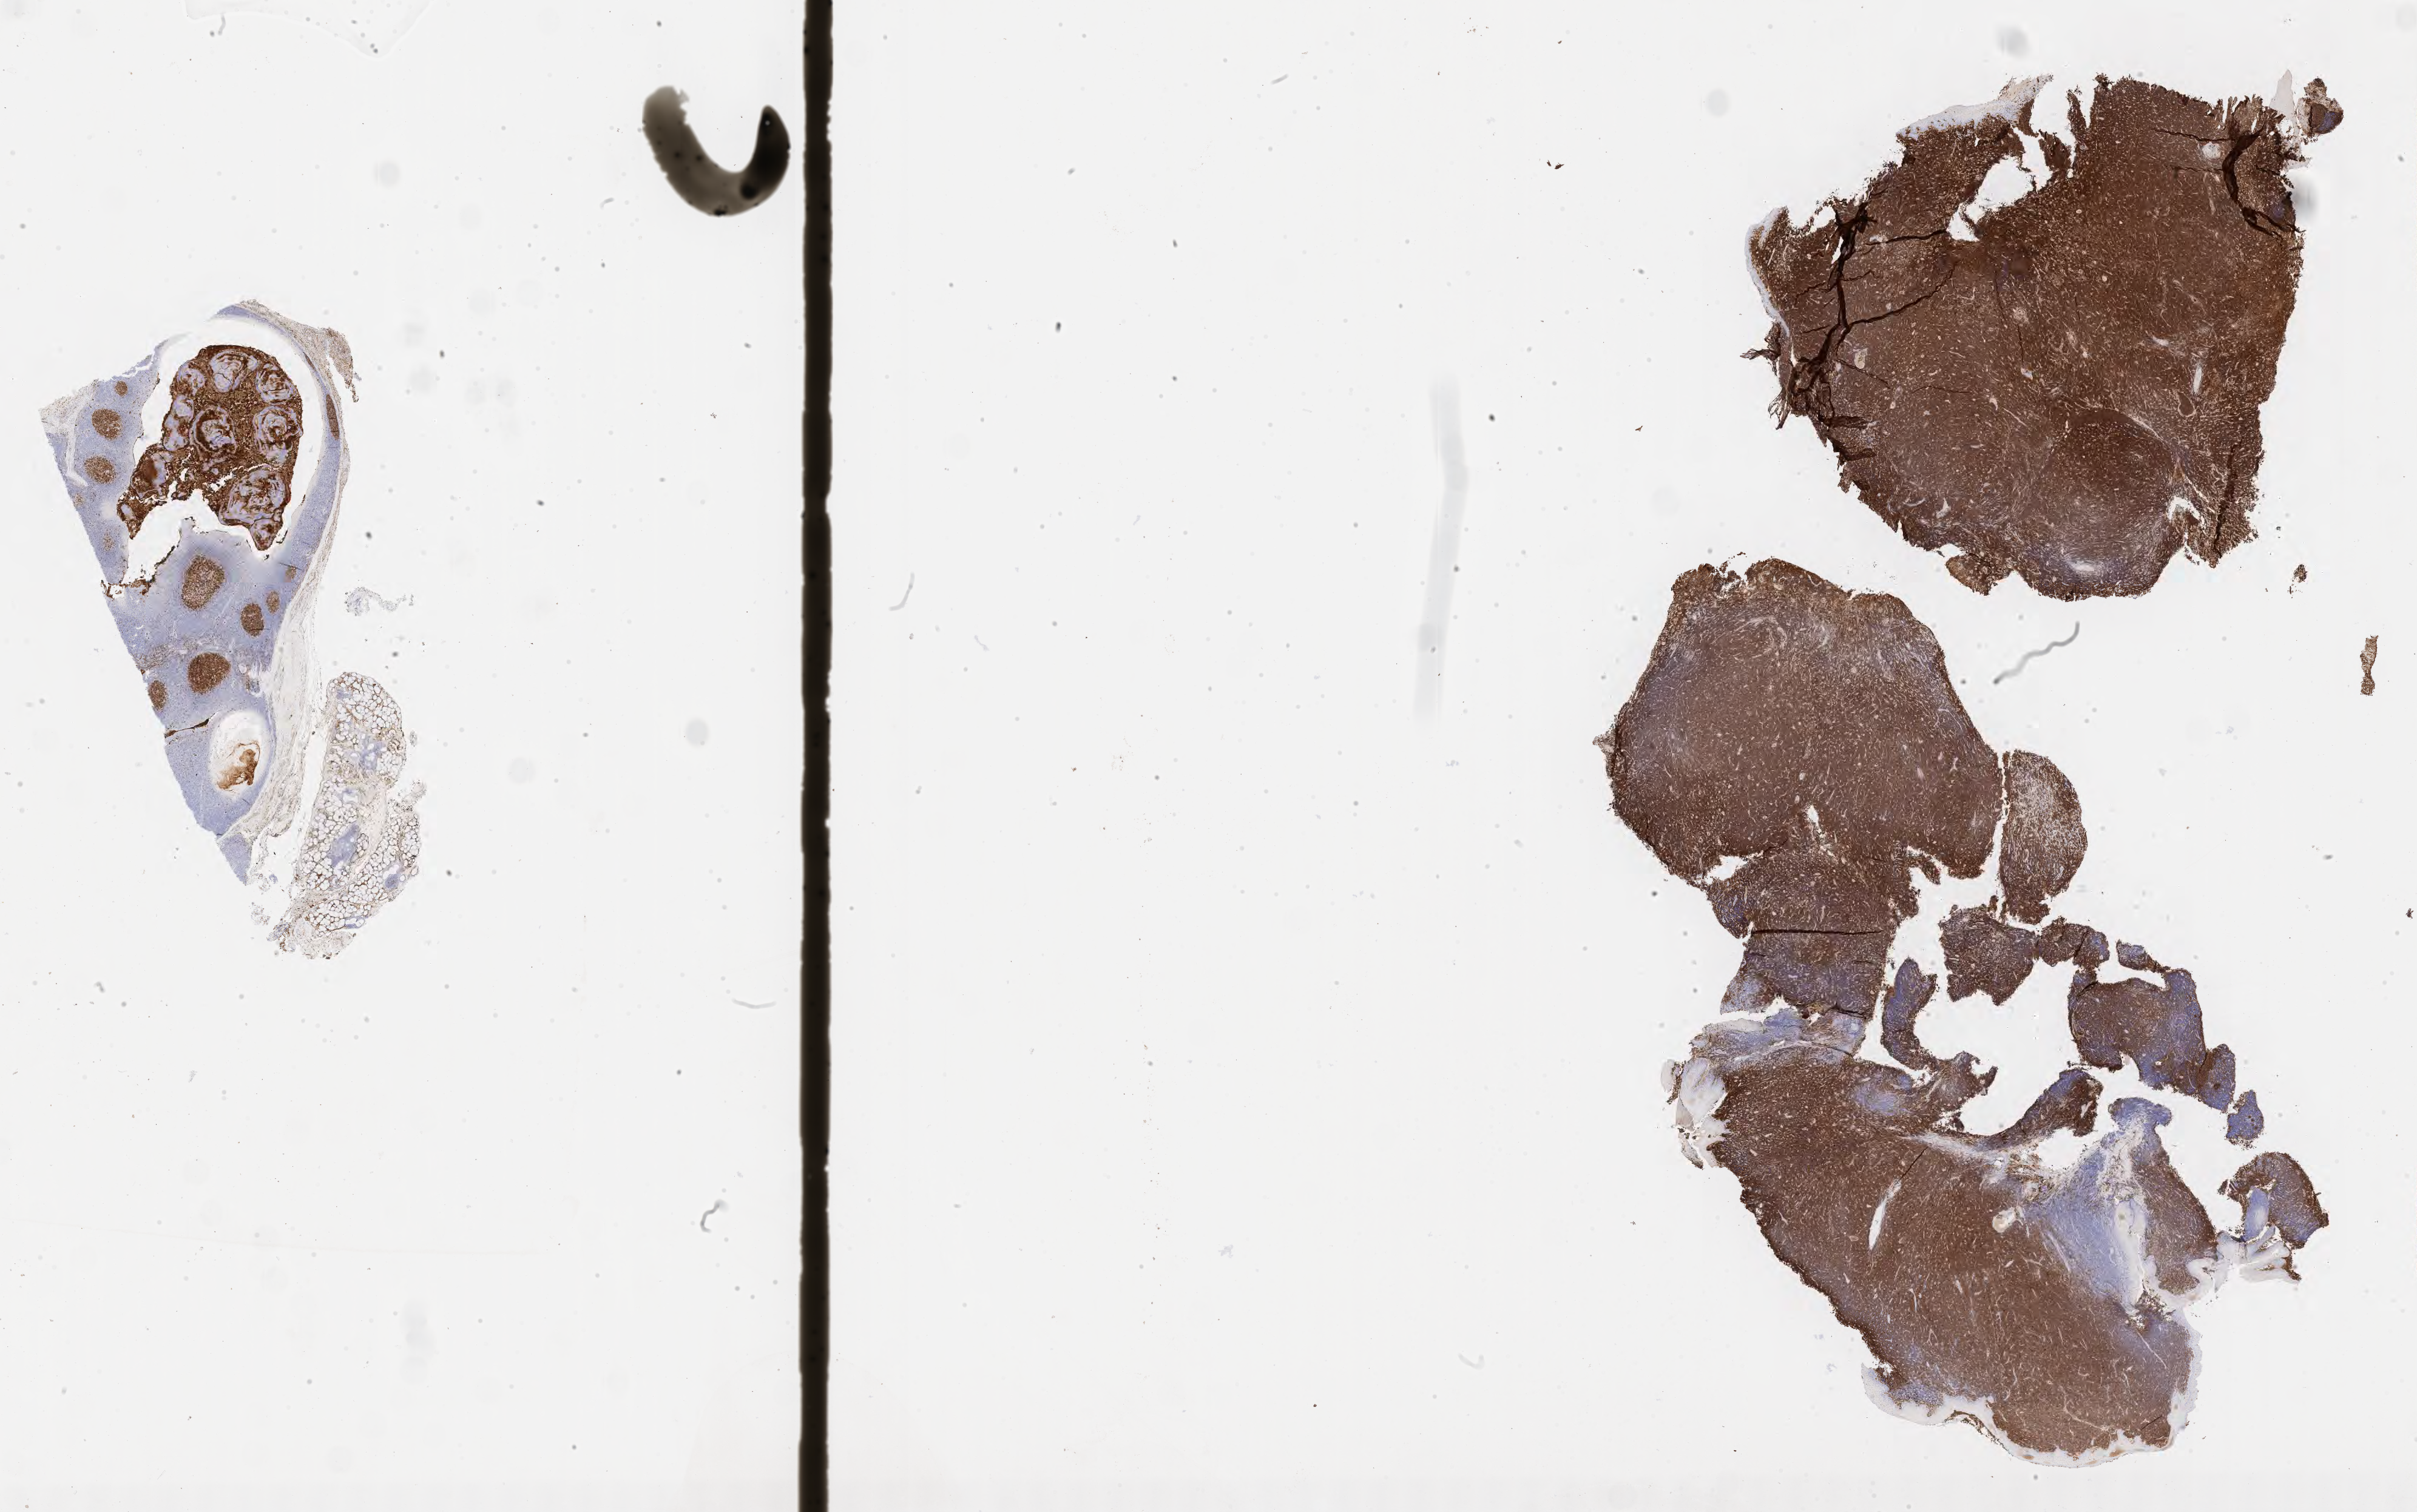
Whole-slide image, immunohistochemical stain for CD10, whole scanned area (about 32.2 x 20.1 mm) shown as a low-resolution overview; specimen: tumor tissue. Male patient, 22 years old.
- diagnosis: Diffuse large B-cell lymphoma, NOS